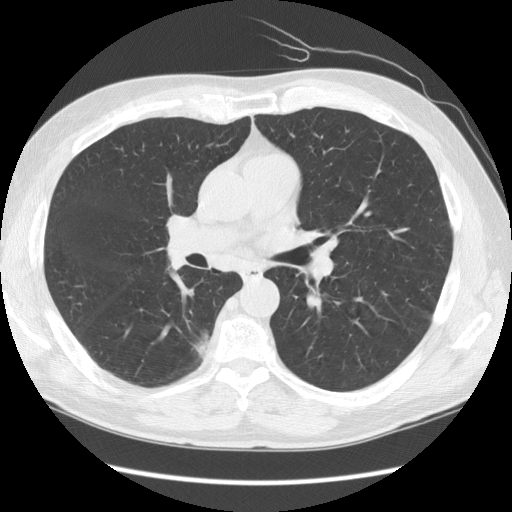
Chest CT (low-dose screening protocol), one axial image, baseline annual screen, lung window (W 1500 / L -600 HU), 2.5 mm slice thickness, slice 59 of 141 in the series. Male, age 69 years at enrolment.
• Lesion marked by an expert reader, bounding box (x1, y1, x2, y2) in pixels: (173, 318, 229, 373).
• Screening reader's record for this exam: no non-calcified nodule ≥4 mm recorded.
• Later outcome: lung cancer diagnosed 497 days after this screen (after the second annual screen) — bronchiolo-alveolar adenocarcinoma, NOS, right lower lobe, well differentiated (G1), stage IB (AJCC 6th edition), 23 mm at pathology.